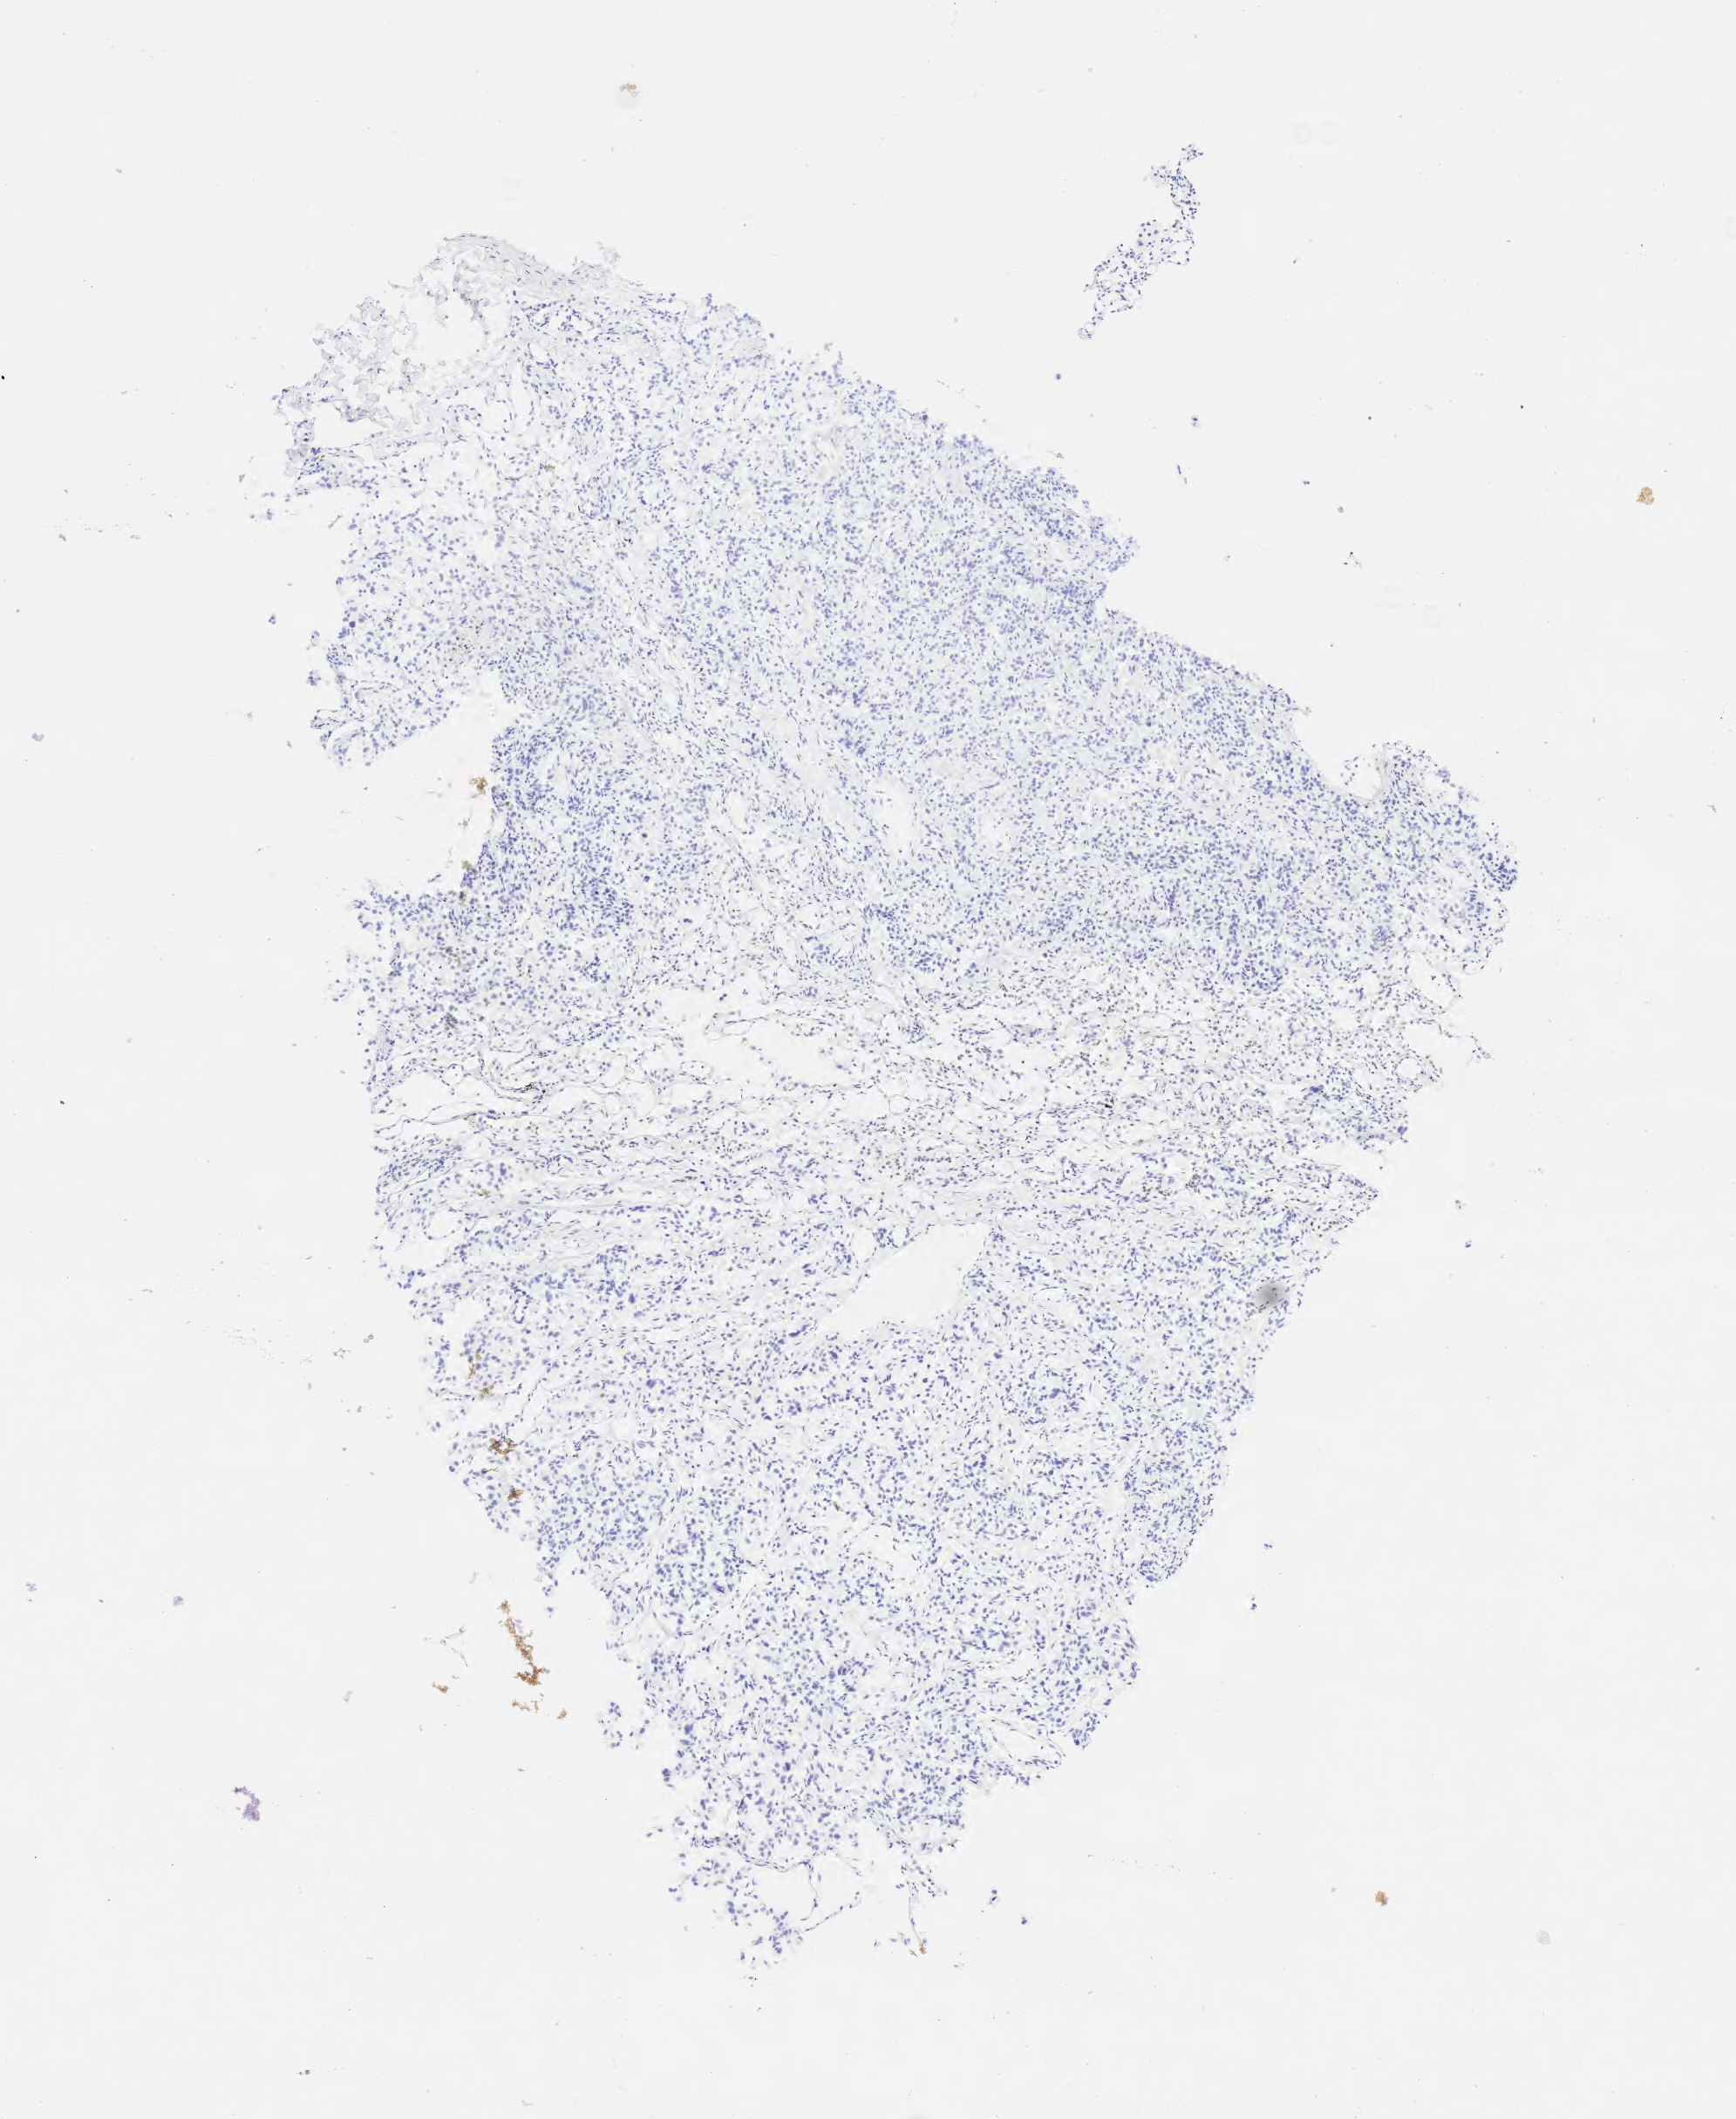
Immunohistochemistry (IHC) whole-slide image stained for TTF-1 (thyroid transcription factor 1) — shown as a low-resolution overview of the whole scanned area (about 4.0 x 4.9 mm), tumor tissue. Male patient.
Histologic diagnosis: Neoplasm, uncertain whether benign or malignant.